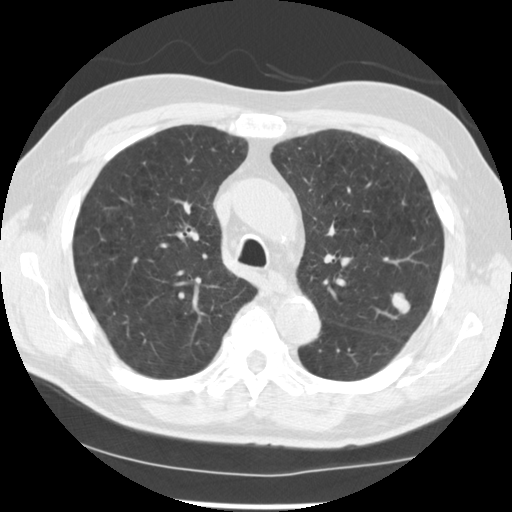
Low-dose screening chest CT, one axial slice. Position 171 of 249 along the scan axis. Reconstruction kernel STANDARD. 120 kVp. Lung window (W 1500 / L -600 HU). 2.5 mm slice thickness. 512 × 512 image matrix.
Annotated regions visible in this slice (expert manual segmentation):
- lesion 1 (tumor, upper lobe of left lung): bounding box <392,293,410,314> (left, top, right, bottom; pixels)